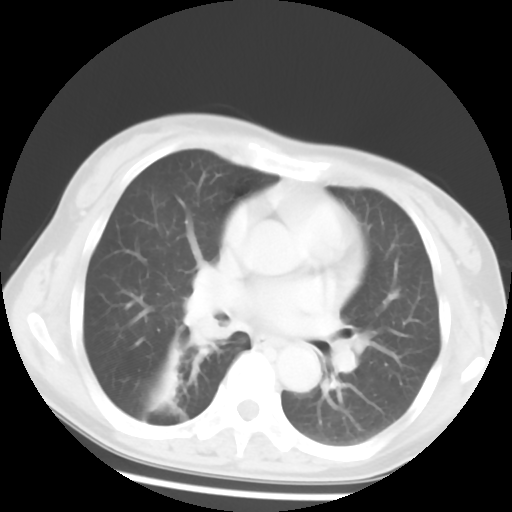
Chest CT, one axial slice; slice 29 of 52 in the series (ordered by position); reconstruction kernel STANDARD; 120 kVp; lung window (W 1500 / L -600 HU); 512 × 512 image matrix, field of view 297 × 297 mm. Patient: female, 54 years. From the clinical record (not read from this slice): clinical TNM (as recorded): T1c N0 M0; histopathological grade: G1-2.
Annotated regions visible in this slice (bounding box drawn by a radiologist):
- lung tumour (recorded histology: squamous cell carcinoma): bounding box [x1, y1, x2, y2] px = [171, 289, 242, 358]